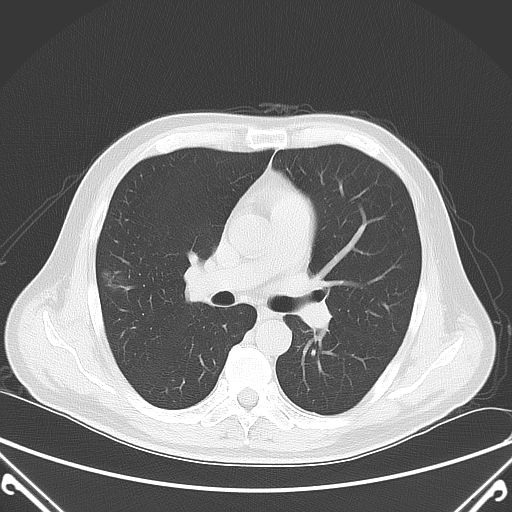
Chest CT, one axial slice. Position 44 of 72 along the scan axis. 120 kVp. Lung window (W 1500 / L -600 HU). 5 mm slice thickness. 512 × 512 image matrix, field of view 380 × 380 mm. Male patient, age 64 years. Case-level facts recorded for this patient, not image findings: clinical TNM (as recorded): T1c N0 M0.
Annotated regions visible in this slice (rectangle marked by the reading radiologist):
- lung tumour (recorded histology: adenocarcinoma): bounding box <95,261,142,303> (left, top, right, bottom; pixels)